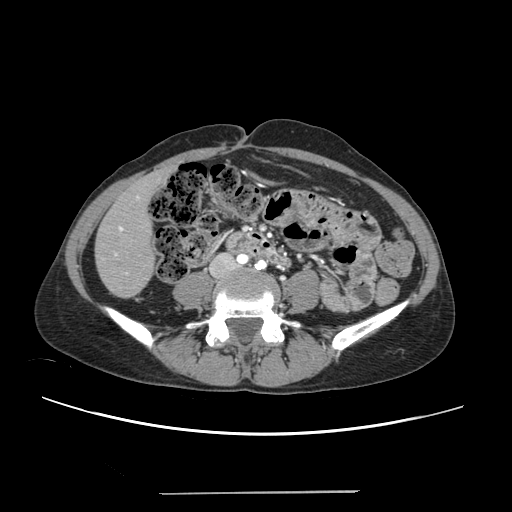
Contrast-enhanced abdominal CT, one axial slice. Position 45 of 240 along the scan axis. 120 kVp. Intravenous contrast given. Soft-tissue window (W 400 / L 40 HU). 1.25 mm slice thickness. 512 × 512 image matrix, field of view 371 × 371 mm. Female patient, age 60 years. Case-level facts recorded for this patient, not image findings: diagnosis: colorectal cancer liver metastases, imaged before liver resection; multiple liver metastases: no; largest metastasis: 1.5 cm; disease in both lobes: no.
Structures marked on this image (outlined manually by an expert reader):
- liver: bounding box (x1, y1, x2, y2) in pixels: (96, 171, 168, 297)
- planned liver remnant (the part of the liver to remain after resection): (96, 172, 166, 297)
- portal vein (with intrahepatic branches): (114, 196, 139, 274)